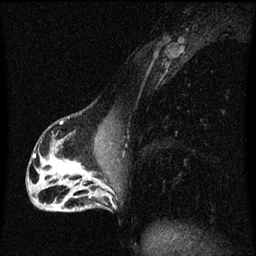
Breast MRI (dynamic contrast-enhanced), one sagittal slice. Position 27 of 60 along the scan axis. Dynamic contrast-enhanced series, image 2 of 3 at this slice position (ordered by acquisition). 1.5 T. TE 4.2 ms, TR 8.4 ms. 2 mm slice thickness. 256 × 256 image matrix, field of view 200 × 200 mm. Patient: female, 40 years.
Annotated regions visible in this slice (semi-automatically segmented with operator editing):
- analysis volume of interest (the breast-tissue region the enhancement analysis was run in; not a lesion): box from (x=76, y=172) to (x=117, y=211) px
- tumour enhancement mask (voxels above the 70 % enhancement threshold inside the analysis volume of interest): (x=76, y=172)–(x=113, y=199)